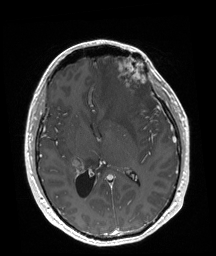
Brain MRI from a brain-tumour surgery series, one axial slice; slice 92 of 192 in the series (ordered by position); T1-weighted post-contrast; 1 mm slice thickness; 216 × 256 image matrix, field of view 219 × 260 mm. From the clinical record (not read from this slice): tumour location: Left Frontal.
Annotated regions visible in this slice (manually delineated by an expert):
- tumour: bounding box [x1, y1, x2, y2] px = [118, 57, 146, 98]